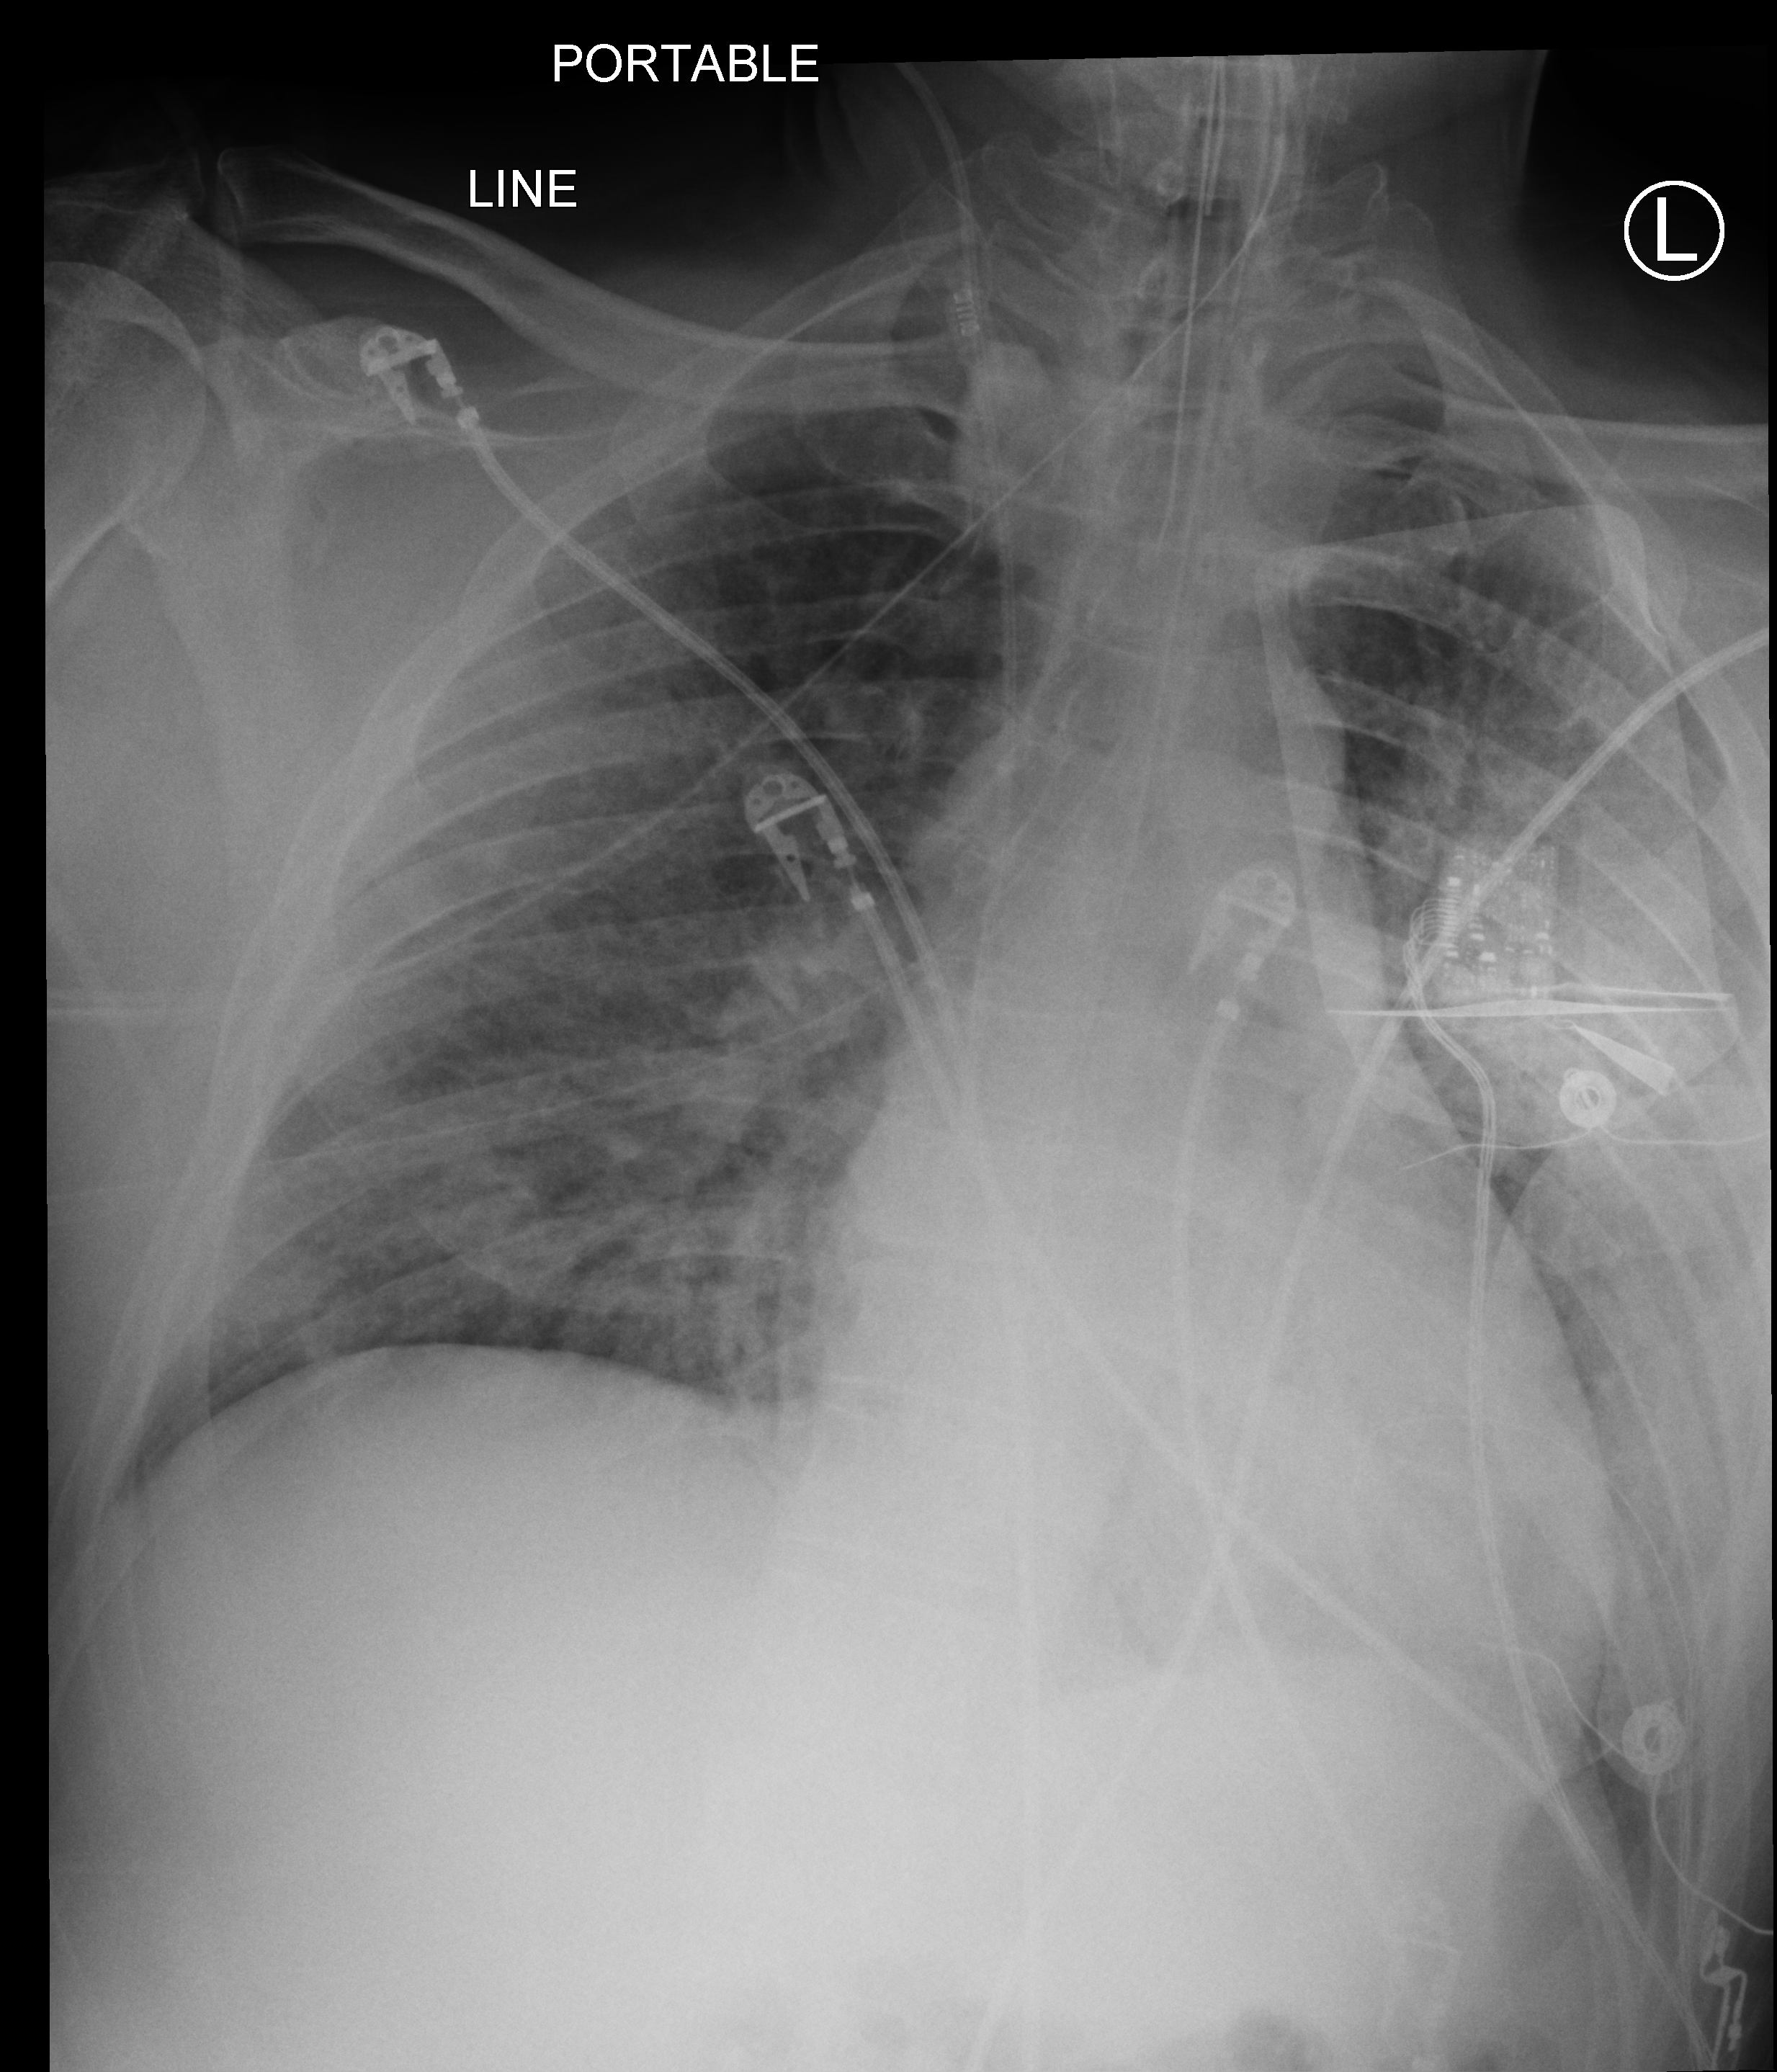
Portable chest radiograph; anteroposterior (AP) projection. Male patient hospitalised with COVID-19, age 18–59 years.
Hospital-stay facts (about this admission, not read from this image; timing relative to this image not recorded):
- mechanically ventilated during this hospital stay: yes
- admitted to intensive care during this hospital stay: yes